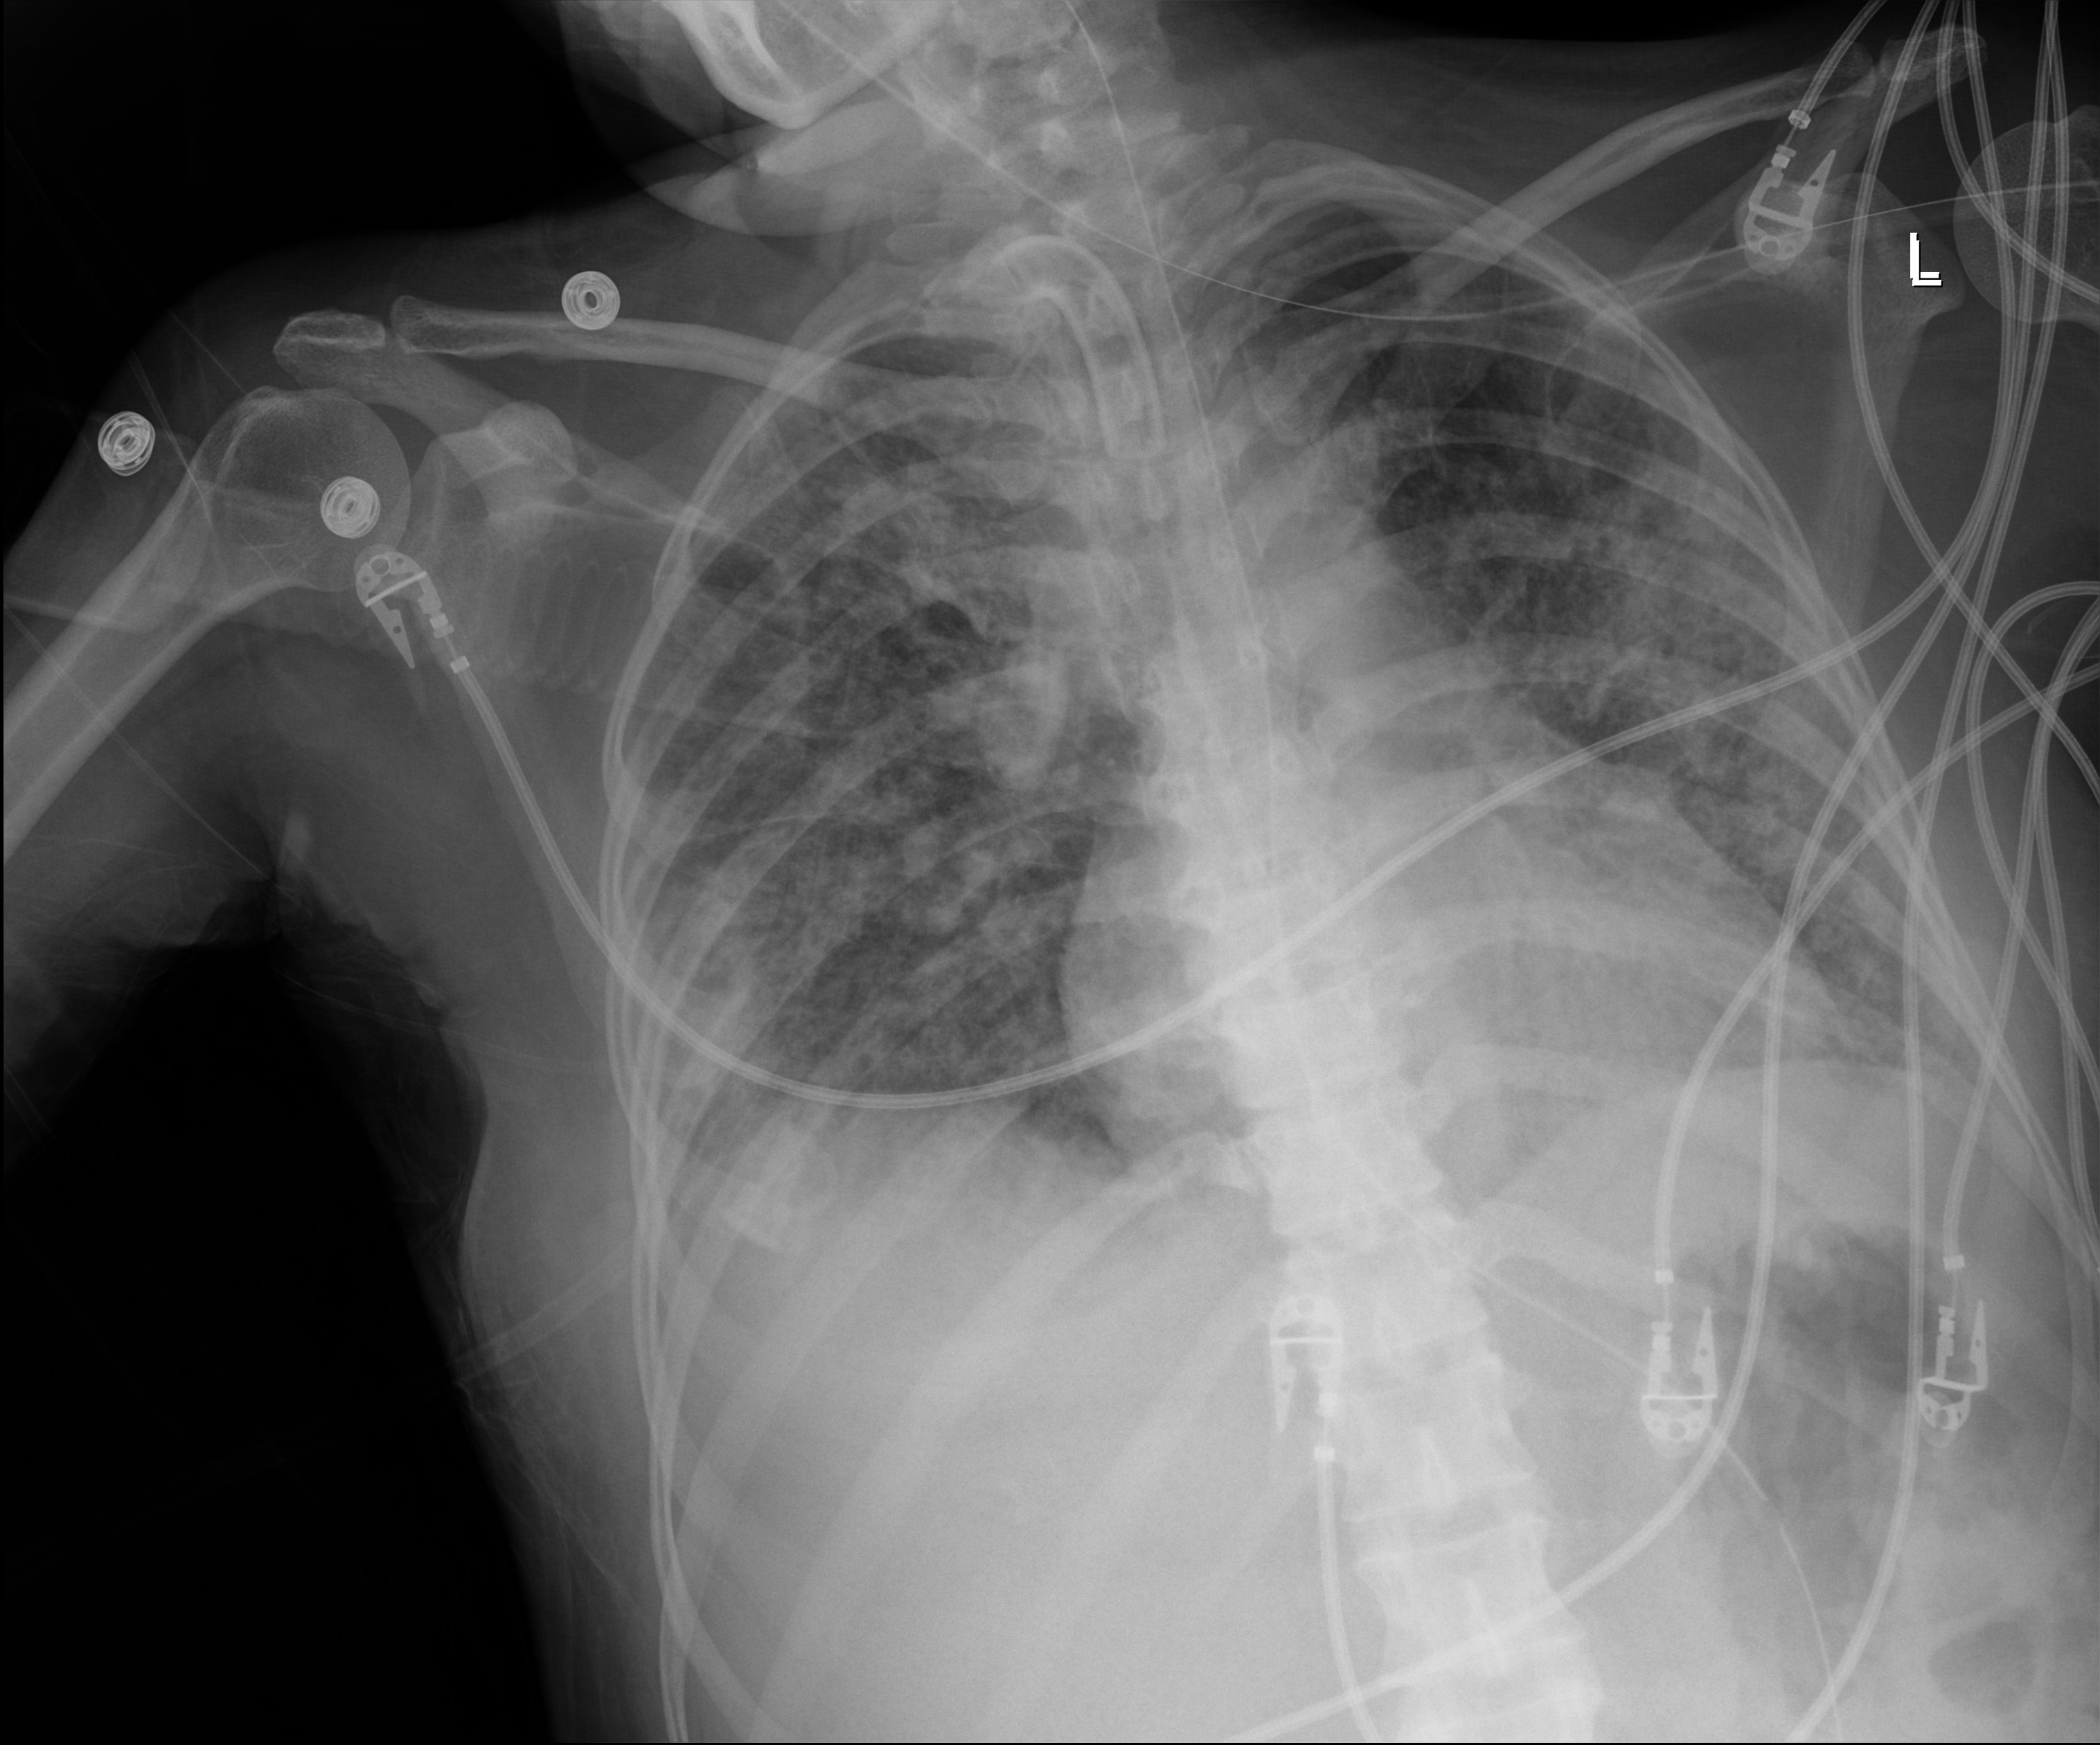
Bedside chest radiograph (digital radiography), anteroposterior (AP) projection. Female patient hospitalised with COVID-19, age 18–59 years.
Hospital-stay facts (about this admission, not read from this image; timing relative to this image not recorded):
- admitted to intensive care during this hospital stay: yes